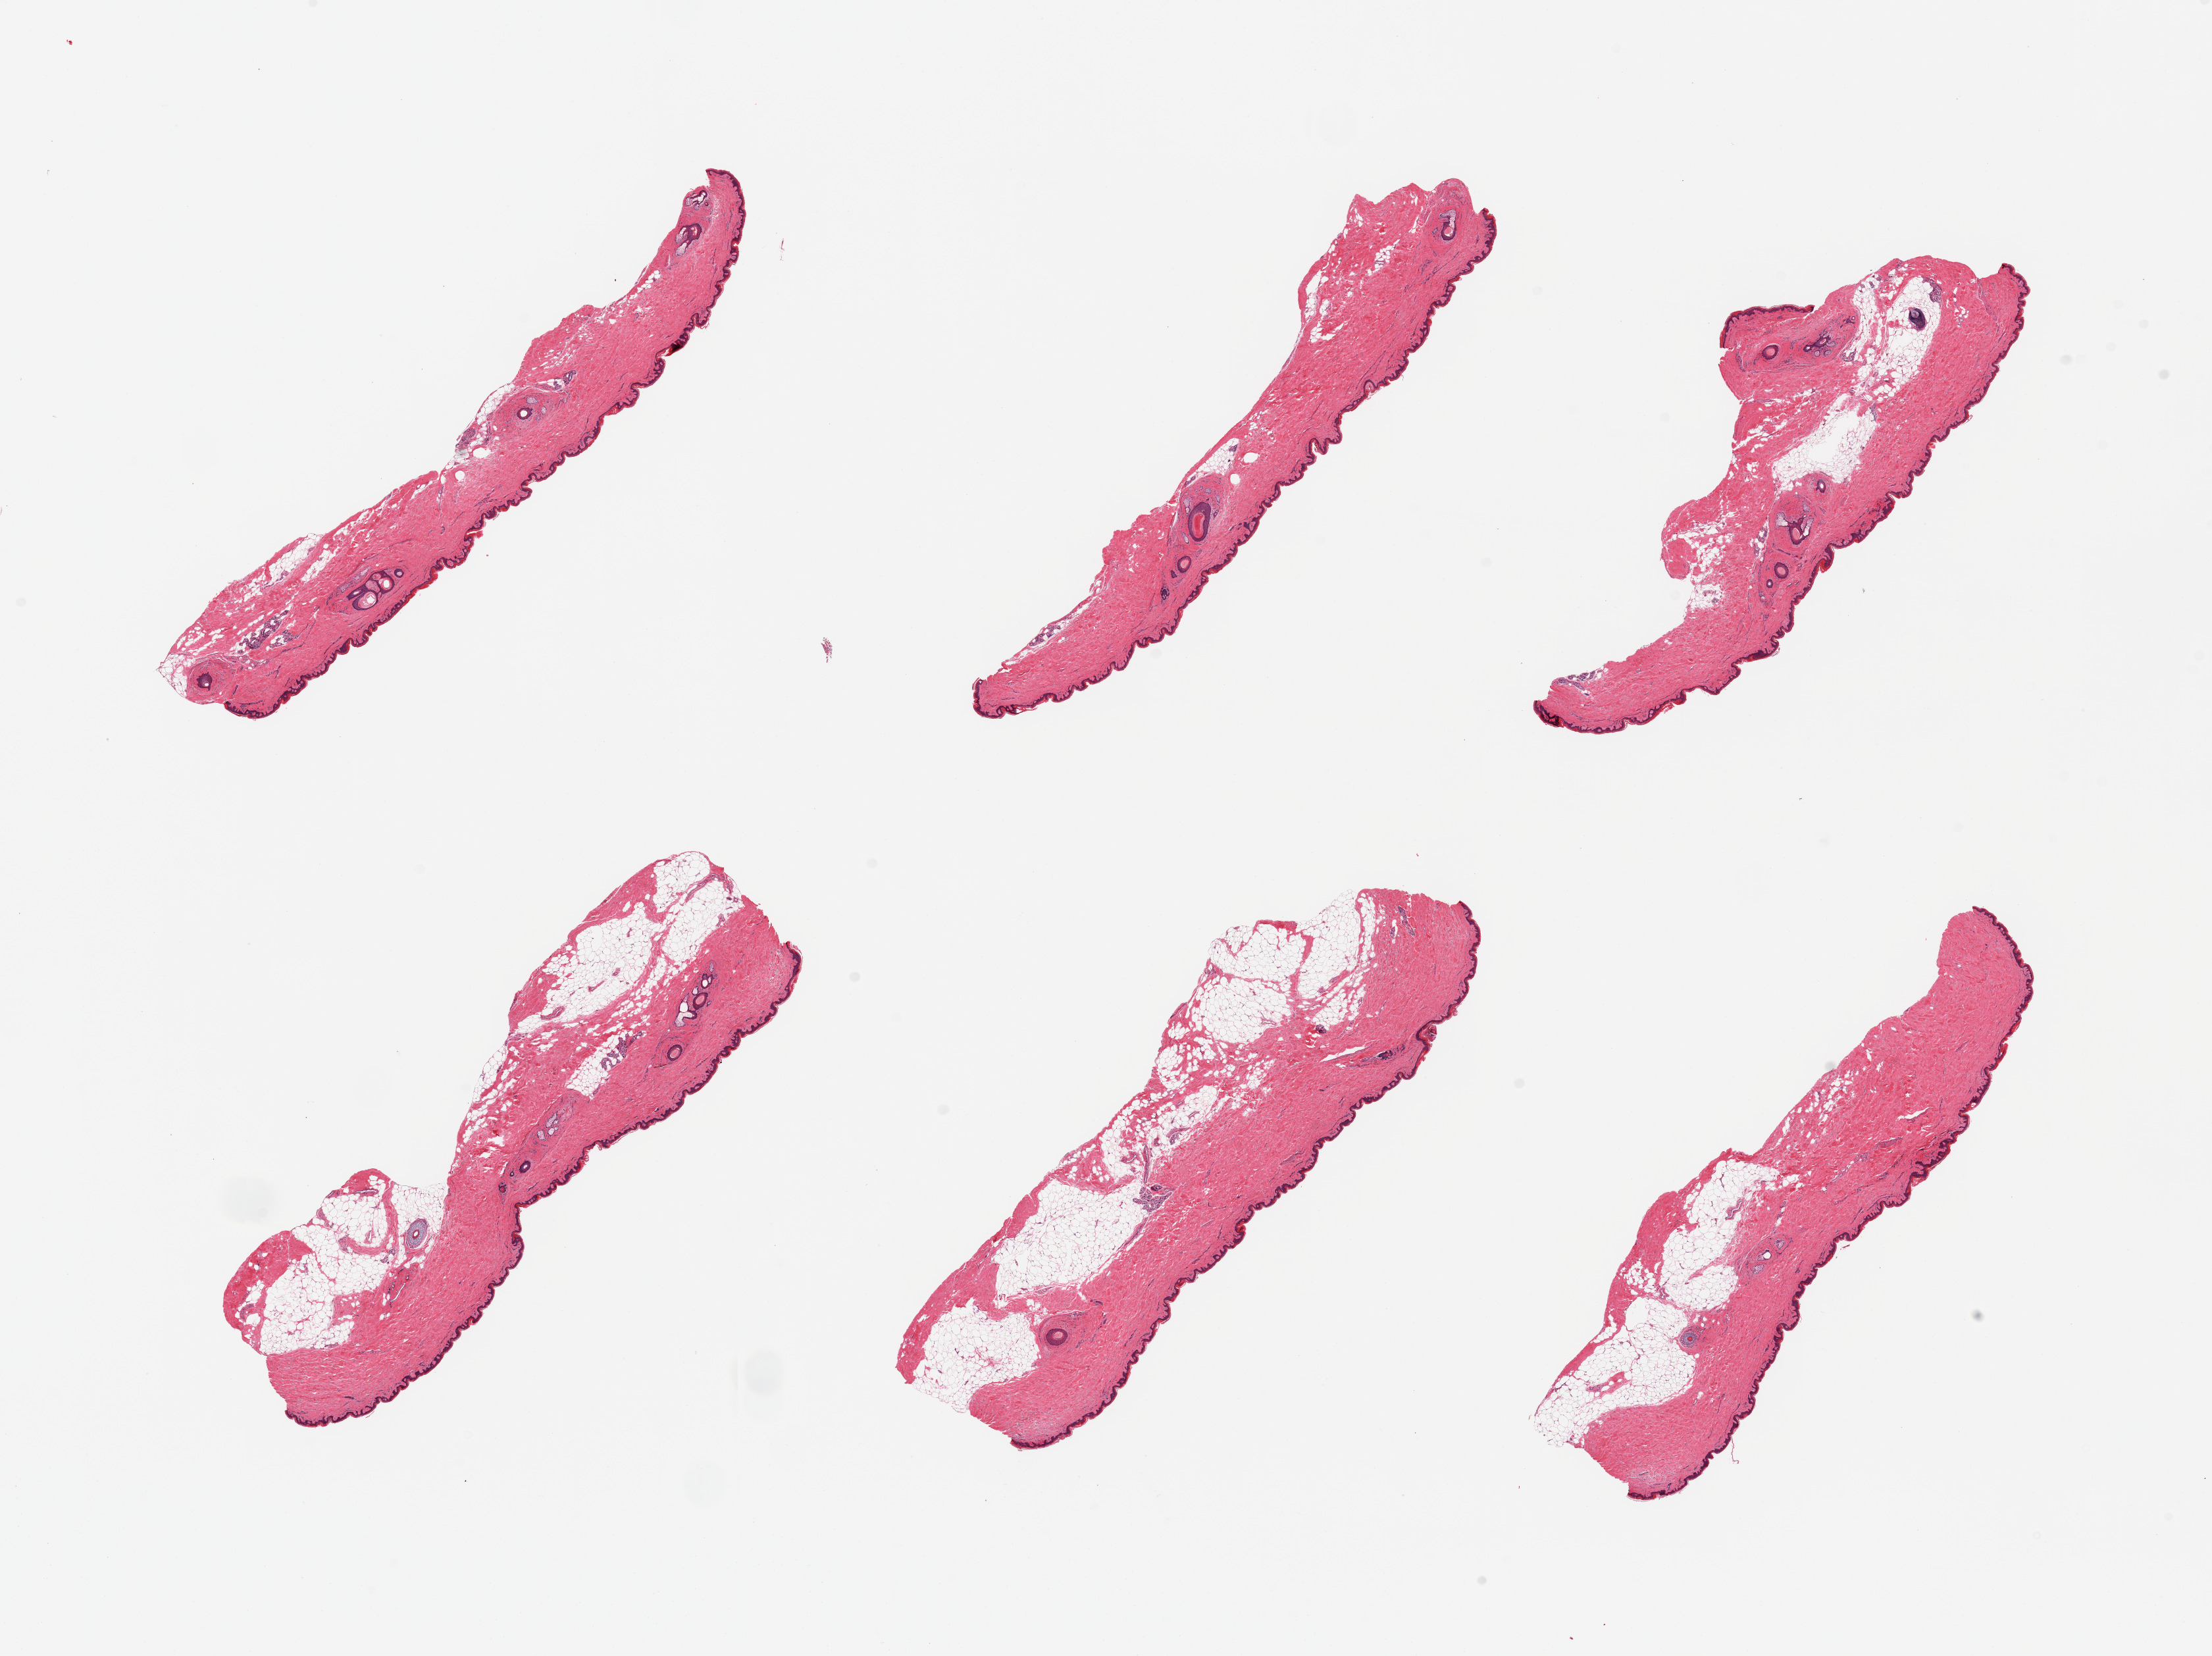
Whole-slide image, H&E stain, shown as a low-resolution overview of the whole scanned area (about 26.6 x 19.9 mm), PAXgene-fixed, paraffin-embedded tissue, sampled site (target tissue): skin of suprapubic region, tissue donor sample. Donor: male.
Pathologist's review note for this sample: 6 pieces; hair bearing skin; 3 pieces with up to 50% external fat, fourth piece with 20% internal fat and remaining two pieces with minimal amount of internal/external fat.